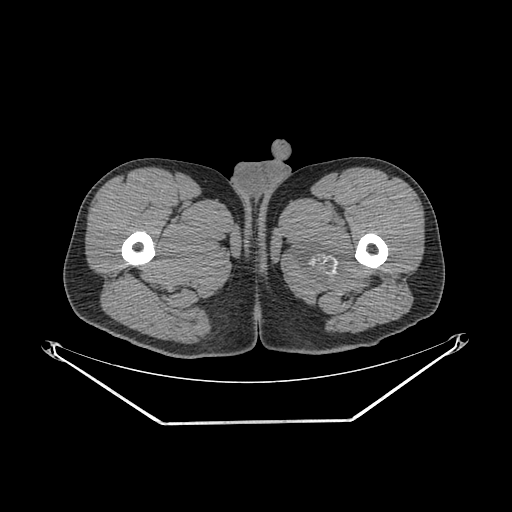
CT of an extremity soft-tissue mass (from a PET/CT study), one axial slice; position 260 of 267 along the scan axis; soft-tissue window (W 400 / L 40 HU); 512 × 512 image matrix, field of view 500 × 500 mm. Male patient. From the clinical record (not read from this slice): histological type: extraskeletal osteosarcoma; grade: high; site of the primary tumour: left adductur.
Annotated regions visible in this slice (expert contour drawn on MRI and transferred to this co-registered scan by the dataset authors):
- gross tumour volume (mass): bounding box <288,209,382,300> (left, top, right, bottom; pixels)